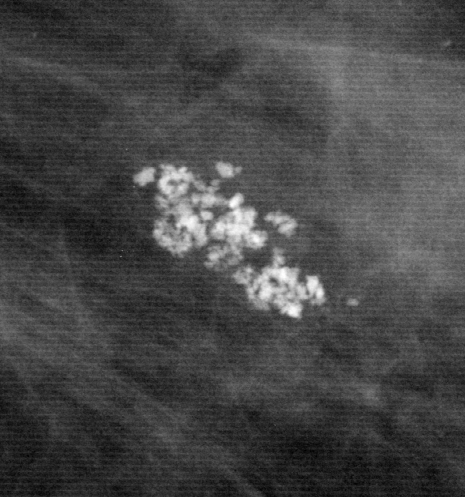
Cropped region of a digitized screen-film mammogram centred on a radiologist-marked abnormality; left breast; CC view.
Finding: calcifications, morphology amorphous, distribution clustered; BI-RADS assessment category 4; pathology (as recorded): benign.